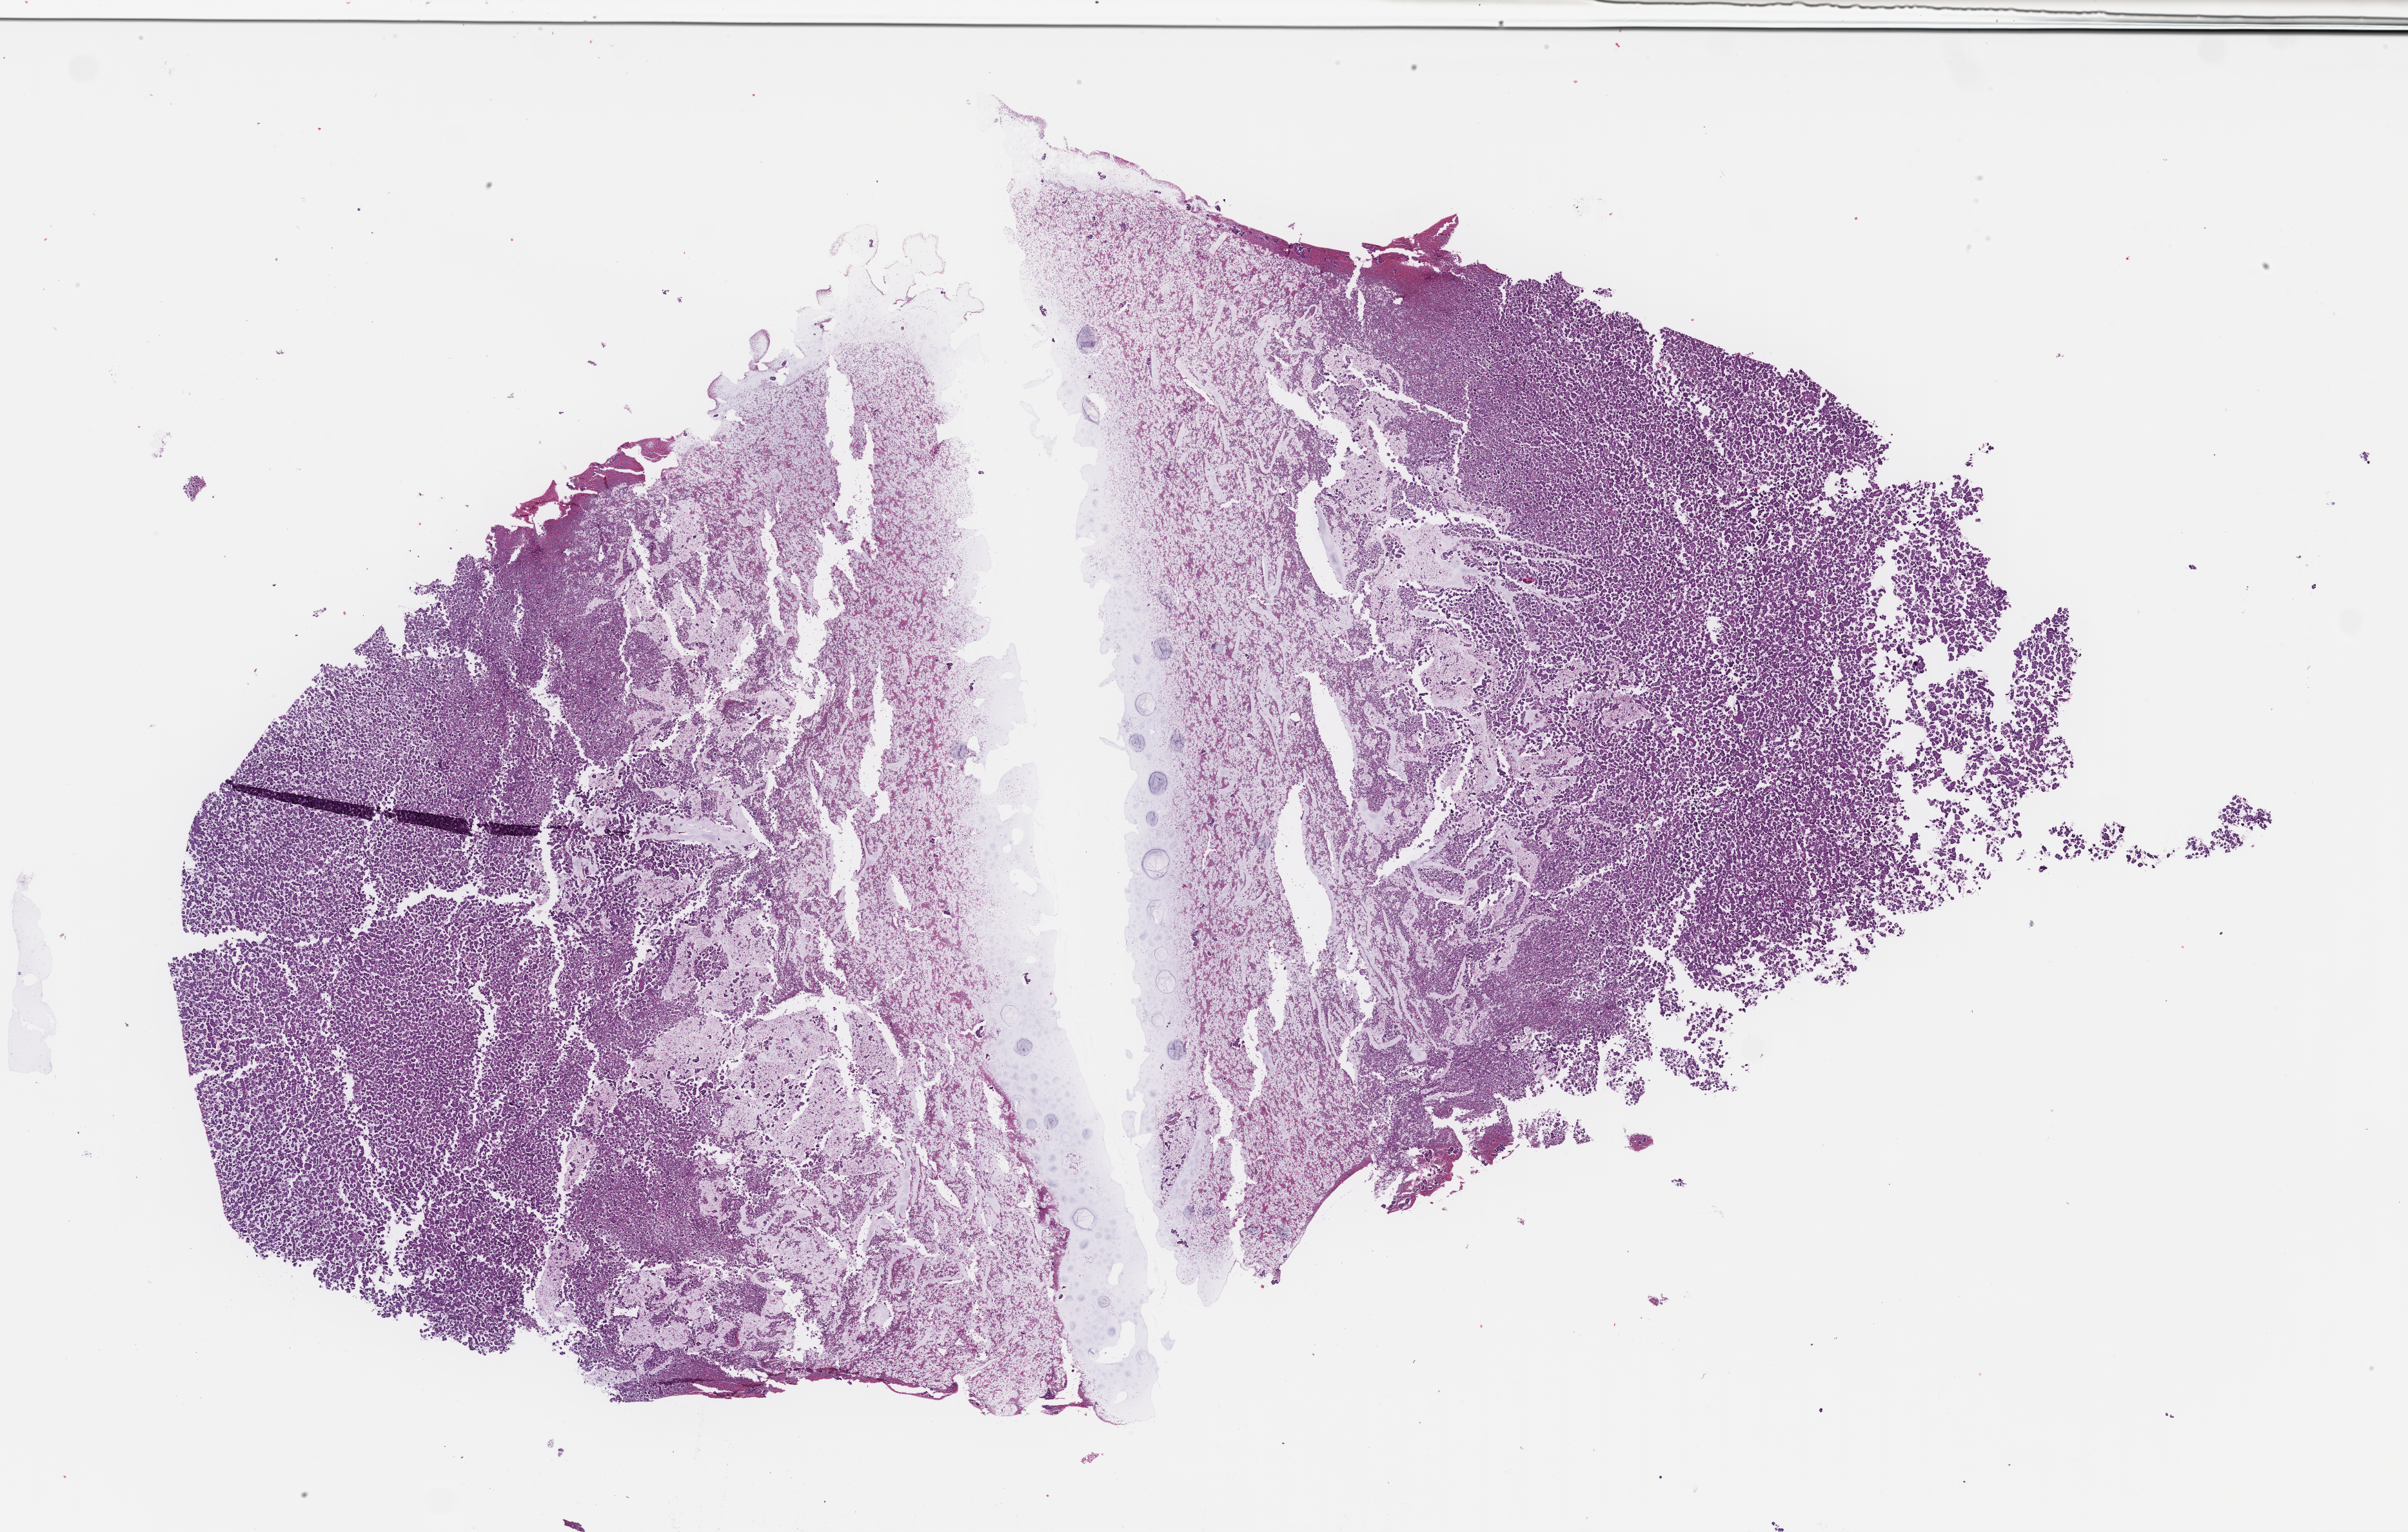
Digitized H&E-stained section, low-resolution overview of the scanned area, about 30.2 x 19.2 mm; formalin-fixed, paraffin-embedded (FFPE) tissue; specimen time point: archival tissue. Patient sex: male.
• this section: metastasis (sampled organ not recorded)
• patient diagnosis (primary): Non-Small Cell Lung Carcinoma